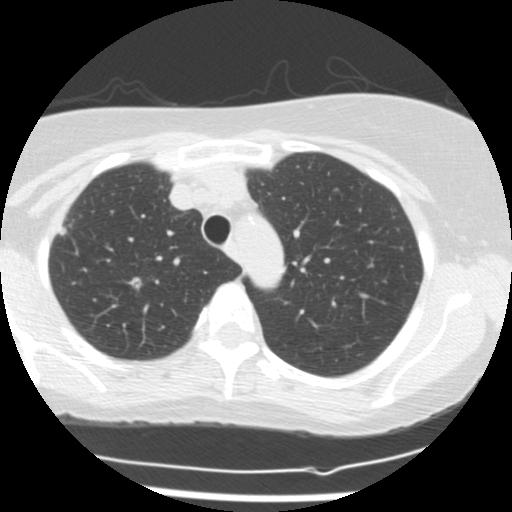
Low-dose screening chest CT, one axial slice. Position 122 of 160 along the scan axis. Lung window (W 1500 / L -600 HU). 2.5 mm slice thickness. 512 × 512 image matrix.
Structures marked on this image (outlined manually by an expert reader):
- lesion 1 (tumor, upper lobe of right lung): bounding box [x1, y1, x2, y2] px = [58, 227, 67, 236]